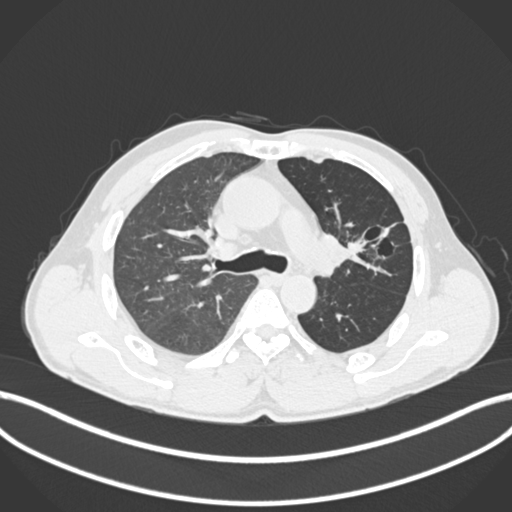
Chest CT, one axial slice; position 125 of 255 along the scan axis; reconstruction kernel B30f; lung window (W 1500 / L -600 HU); 1 mm slice thickness; 512 × 512 image matrix, field of view 400 × 400 mm. Male patient, age 57 years. From the clinical record (not read from this slice): clinical TNM (as recorded): T2b N0 M0.
Annotated regions visible in this slice (bounding box drawn by a radiologist):
- lung tumour (recorded histology: squamous cell carcinoma): box from (x=316, y=226) to (x=365, y=276) px